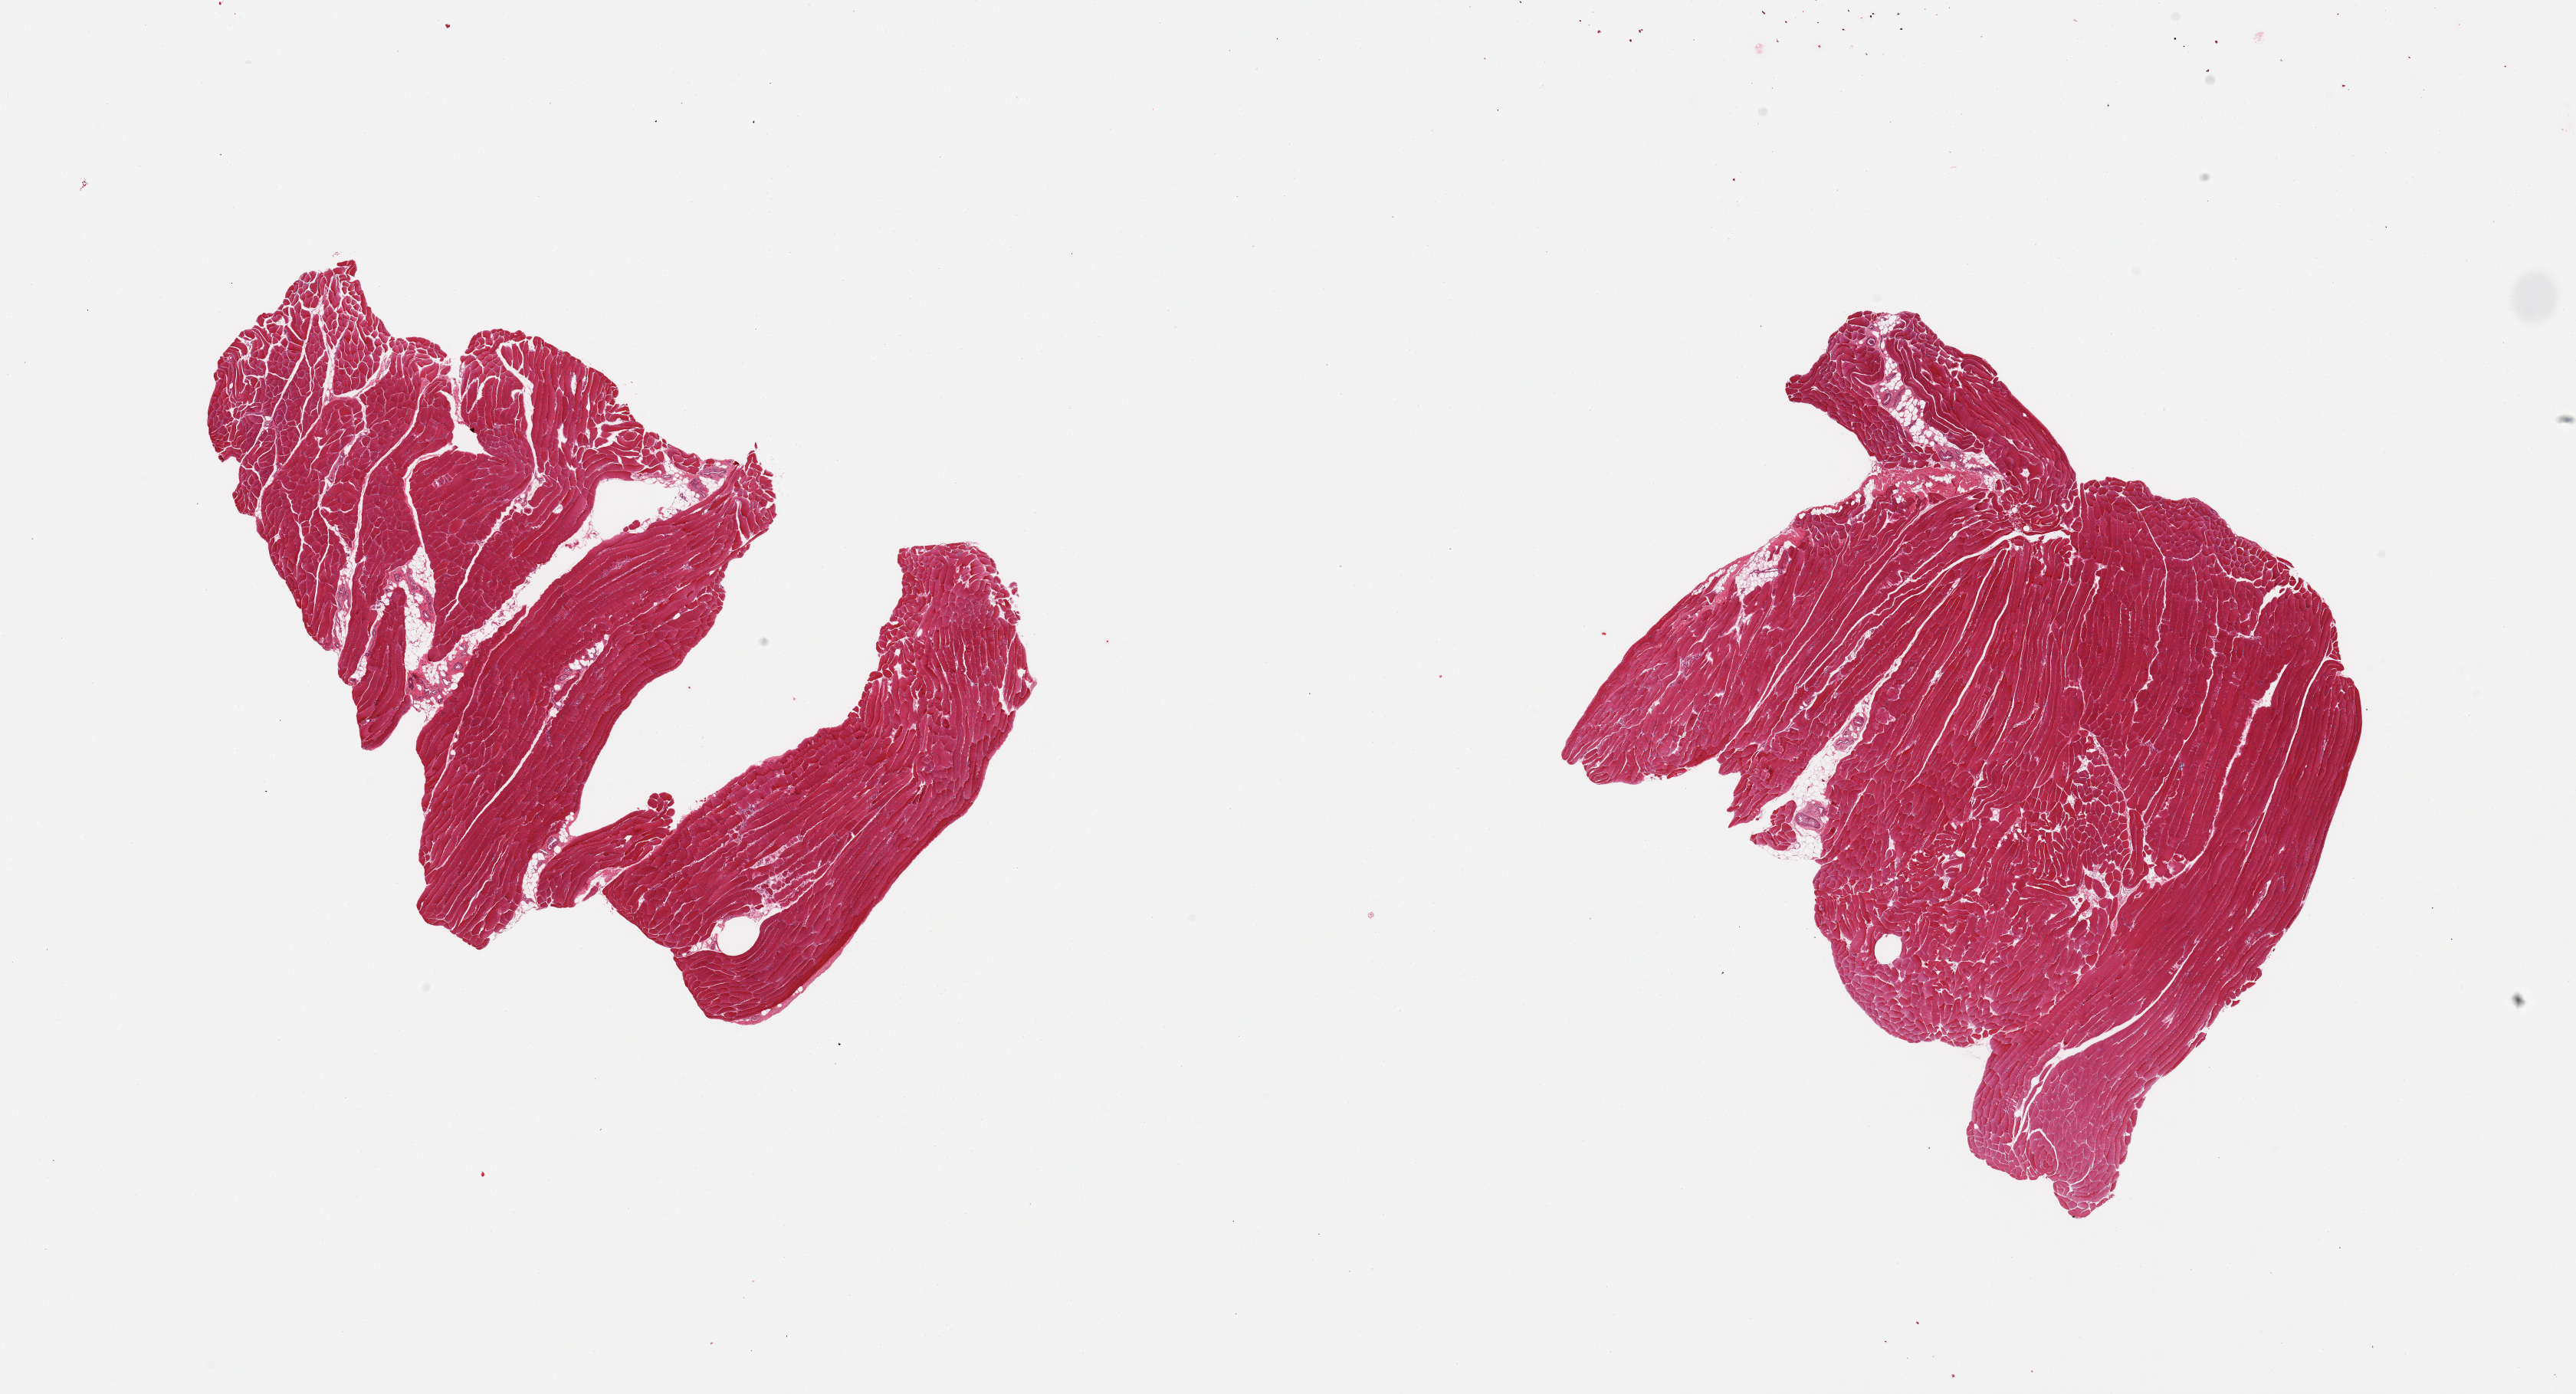
Whole-slide image, haematoxylin and eosin stain, shown as a low-resolution overview of the whole scanned area (about 26.6 x 14.4 mm). PAXgene-fixed paraffin-embedded (PFPE) section. Sampled site (target tissue): skeletal muscle. Tissue donor sample. Donor sex: male.
- review note (as recorded): 2 pieces; ~5% internal fat